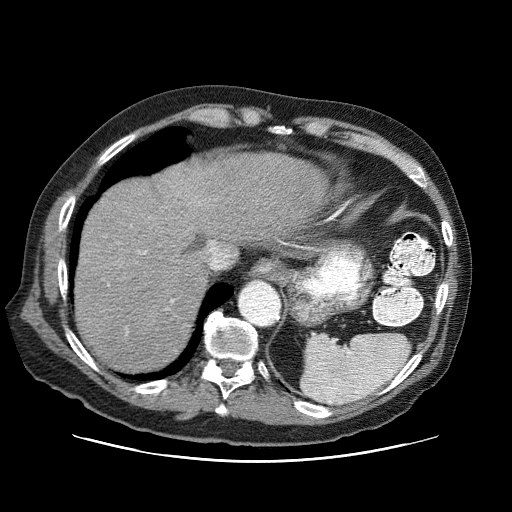
Contrast-enhanced abdominal CT (liver protocol), one axial slice. Slice 62 of 87 in the series (ordered by position). Reconstruction kernel STANDARD. One of 3 acquisitions stored at this slice position. Soft-tissue window (W 400 / L 40 HU). 2.5 mm slice thickness. 512 × 512 image matrix, field of view 400 × 400 mm. From the clinical record (not read from this slice): diagnosis: hepatocellular carcinoma (patient treated with transarterial chemoembolisation; whether this scan precedes or follows treatment is not stated here); TNM stage (as recorded): Stage-IIIA; Child-Pugh class: A.
Annotated regions visible in this slice (semi-automatic segmentation, software-assisted and operator-edited):
- liver parenchyma outside the tumour (the mass and vessels are separate outlines, so this box may not span the whole liver): bounding box (x1, y1, x2, y2) in pixels: (74, 152, 326, 372)
- liver vessels: (144, 252, 174, 302)